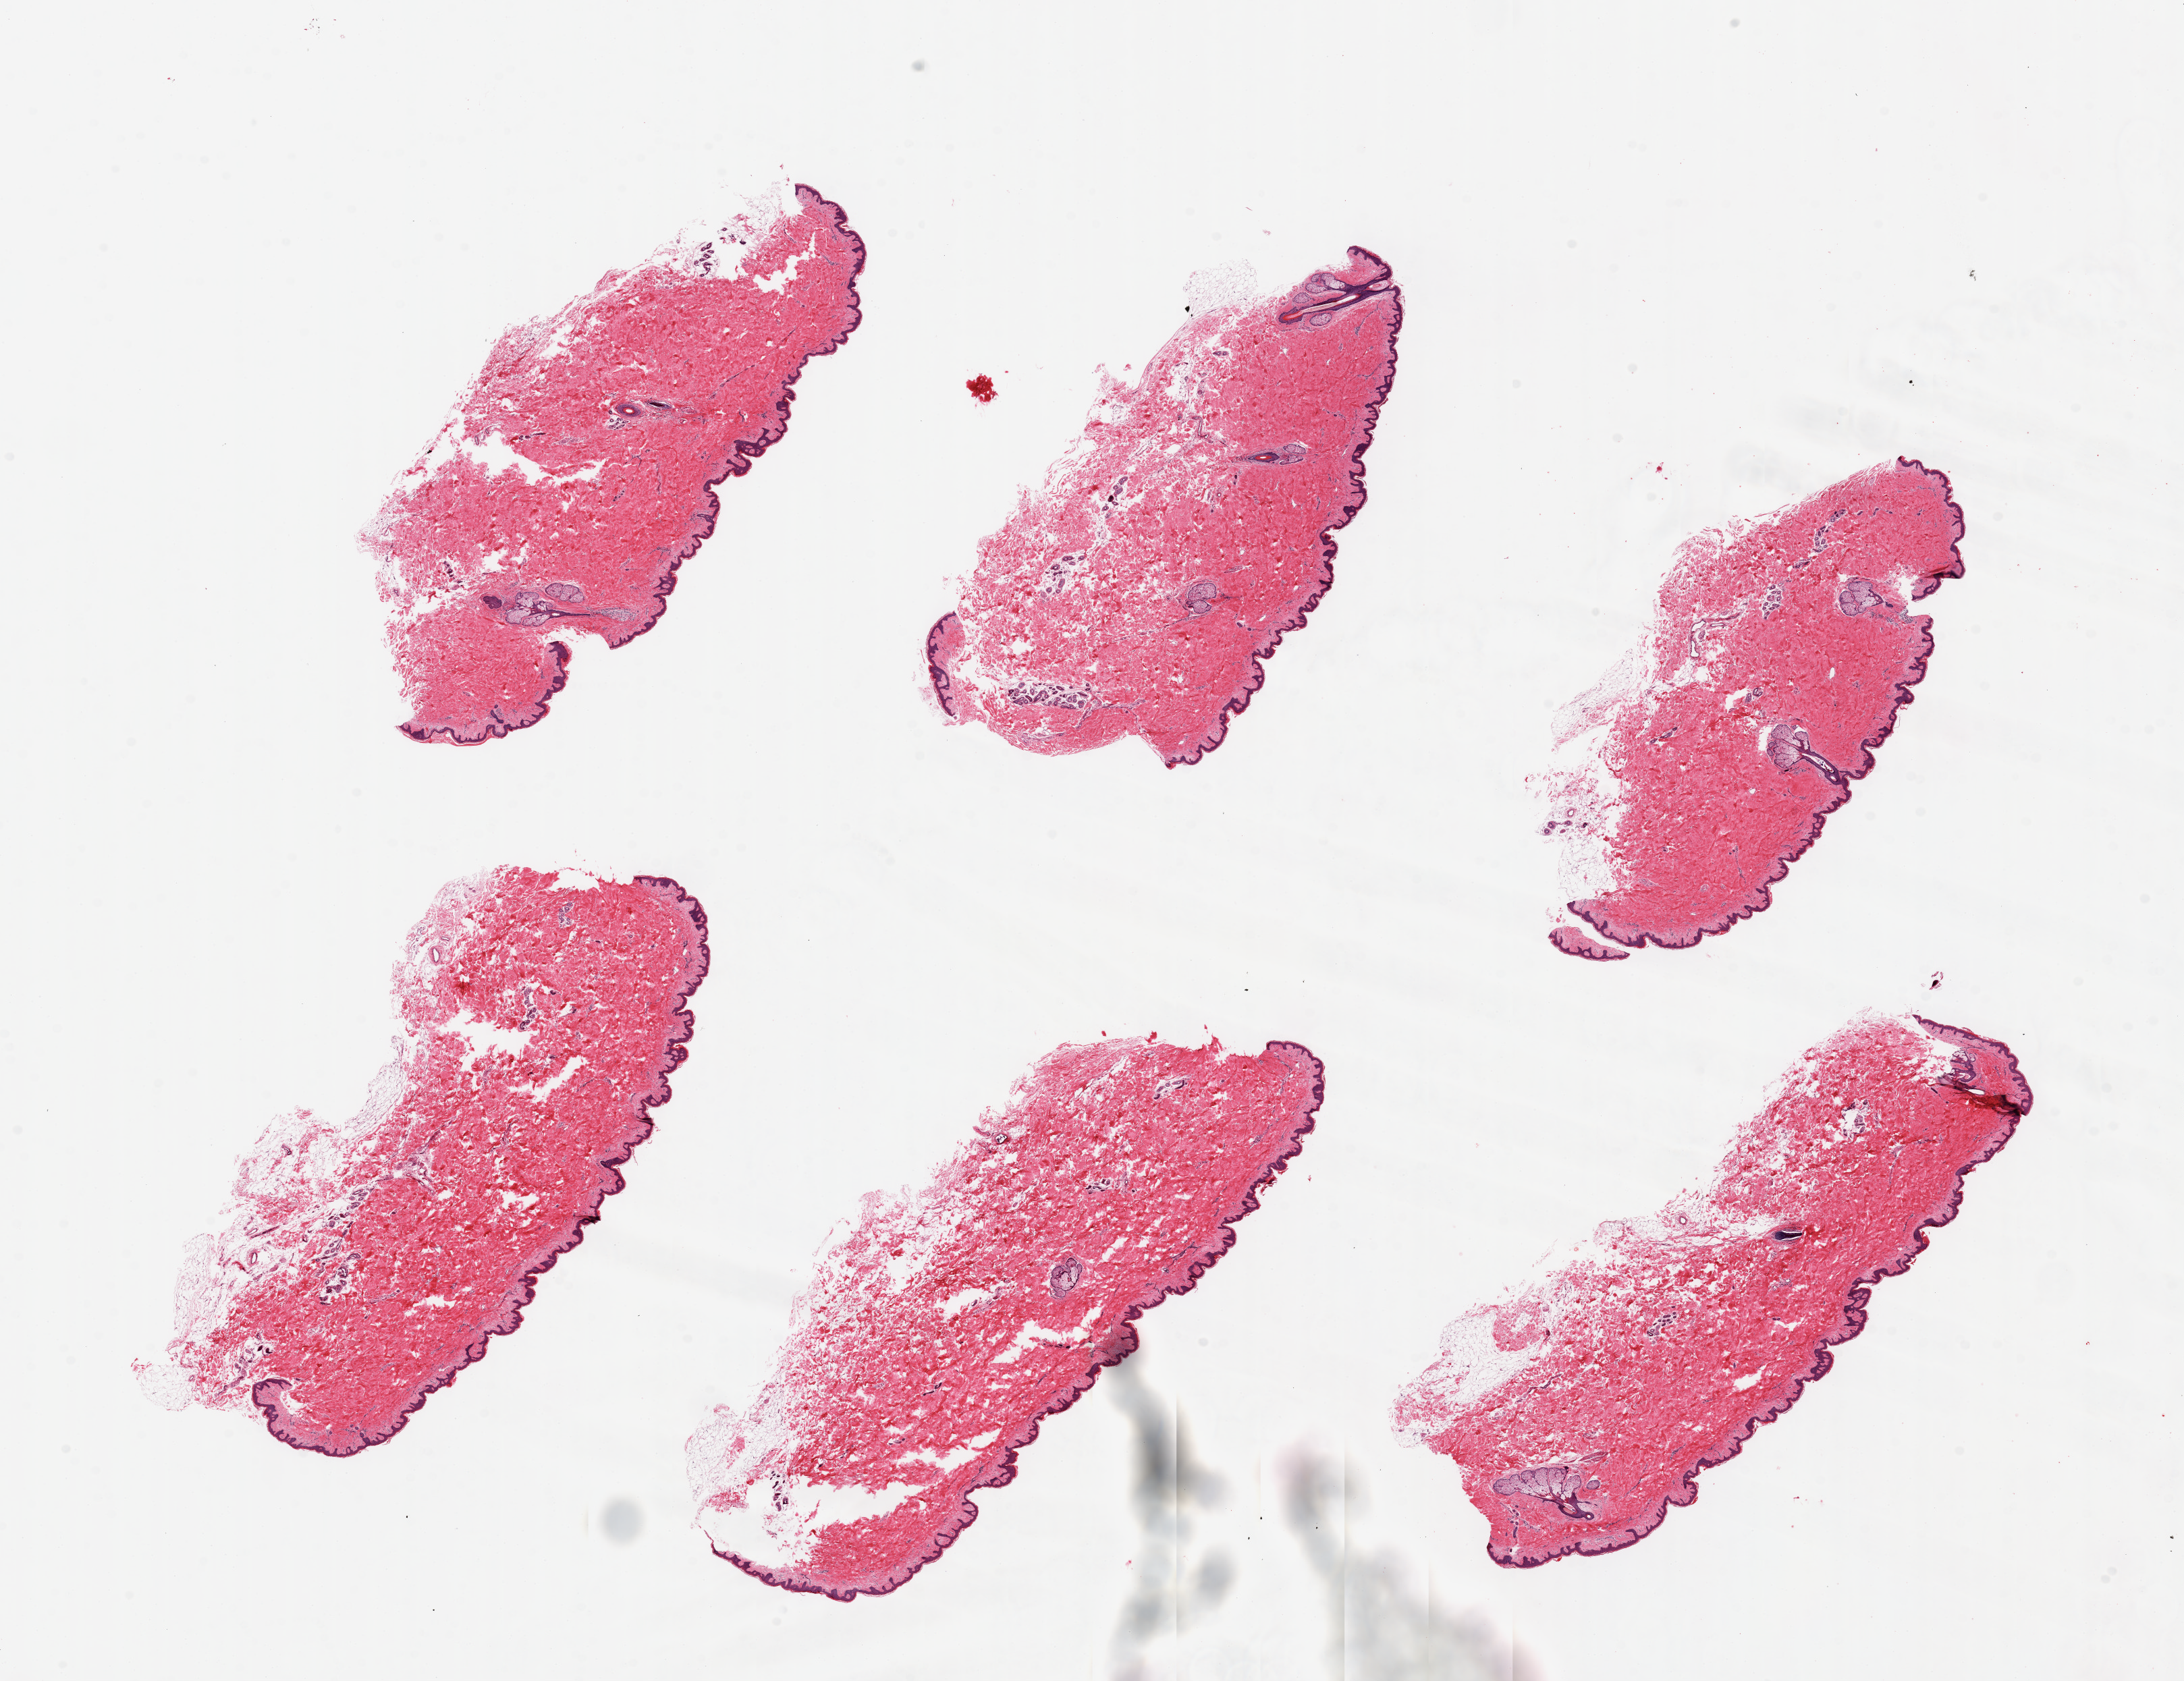
Whole-slide image, H&E stain, brightfield — shown as a low-resolution overview of the whole scanned area (about 25.6 x 19.7 mm). PAXgene-fixed, paraffin-embedded tissue. Sampled site (target tissue): skin of suprapubic region. Donor tissue sample. Donor sex: female.
- review note (as recorded): 6 pieces, up to 9x4mm; well trimmed subcutaneous fat